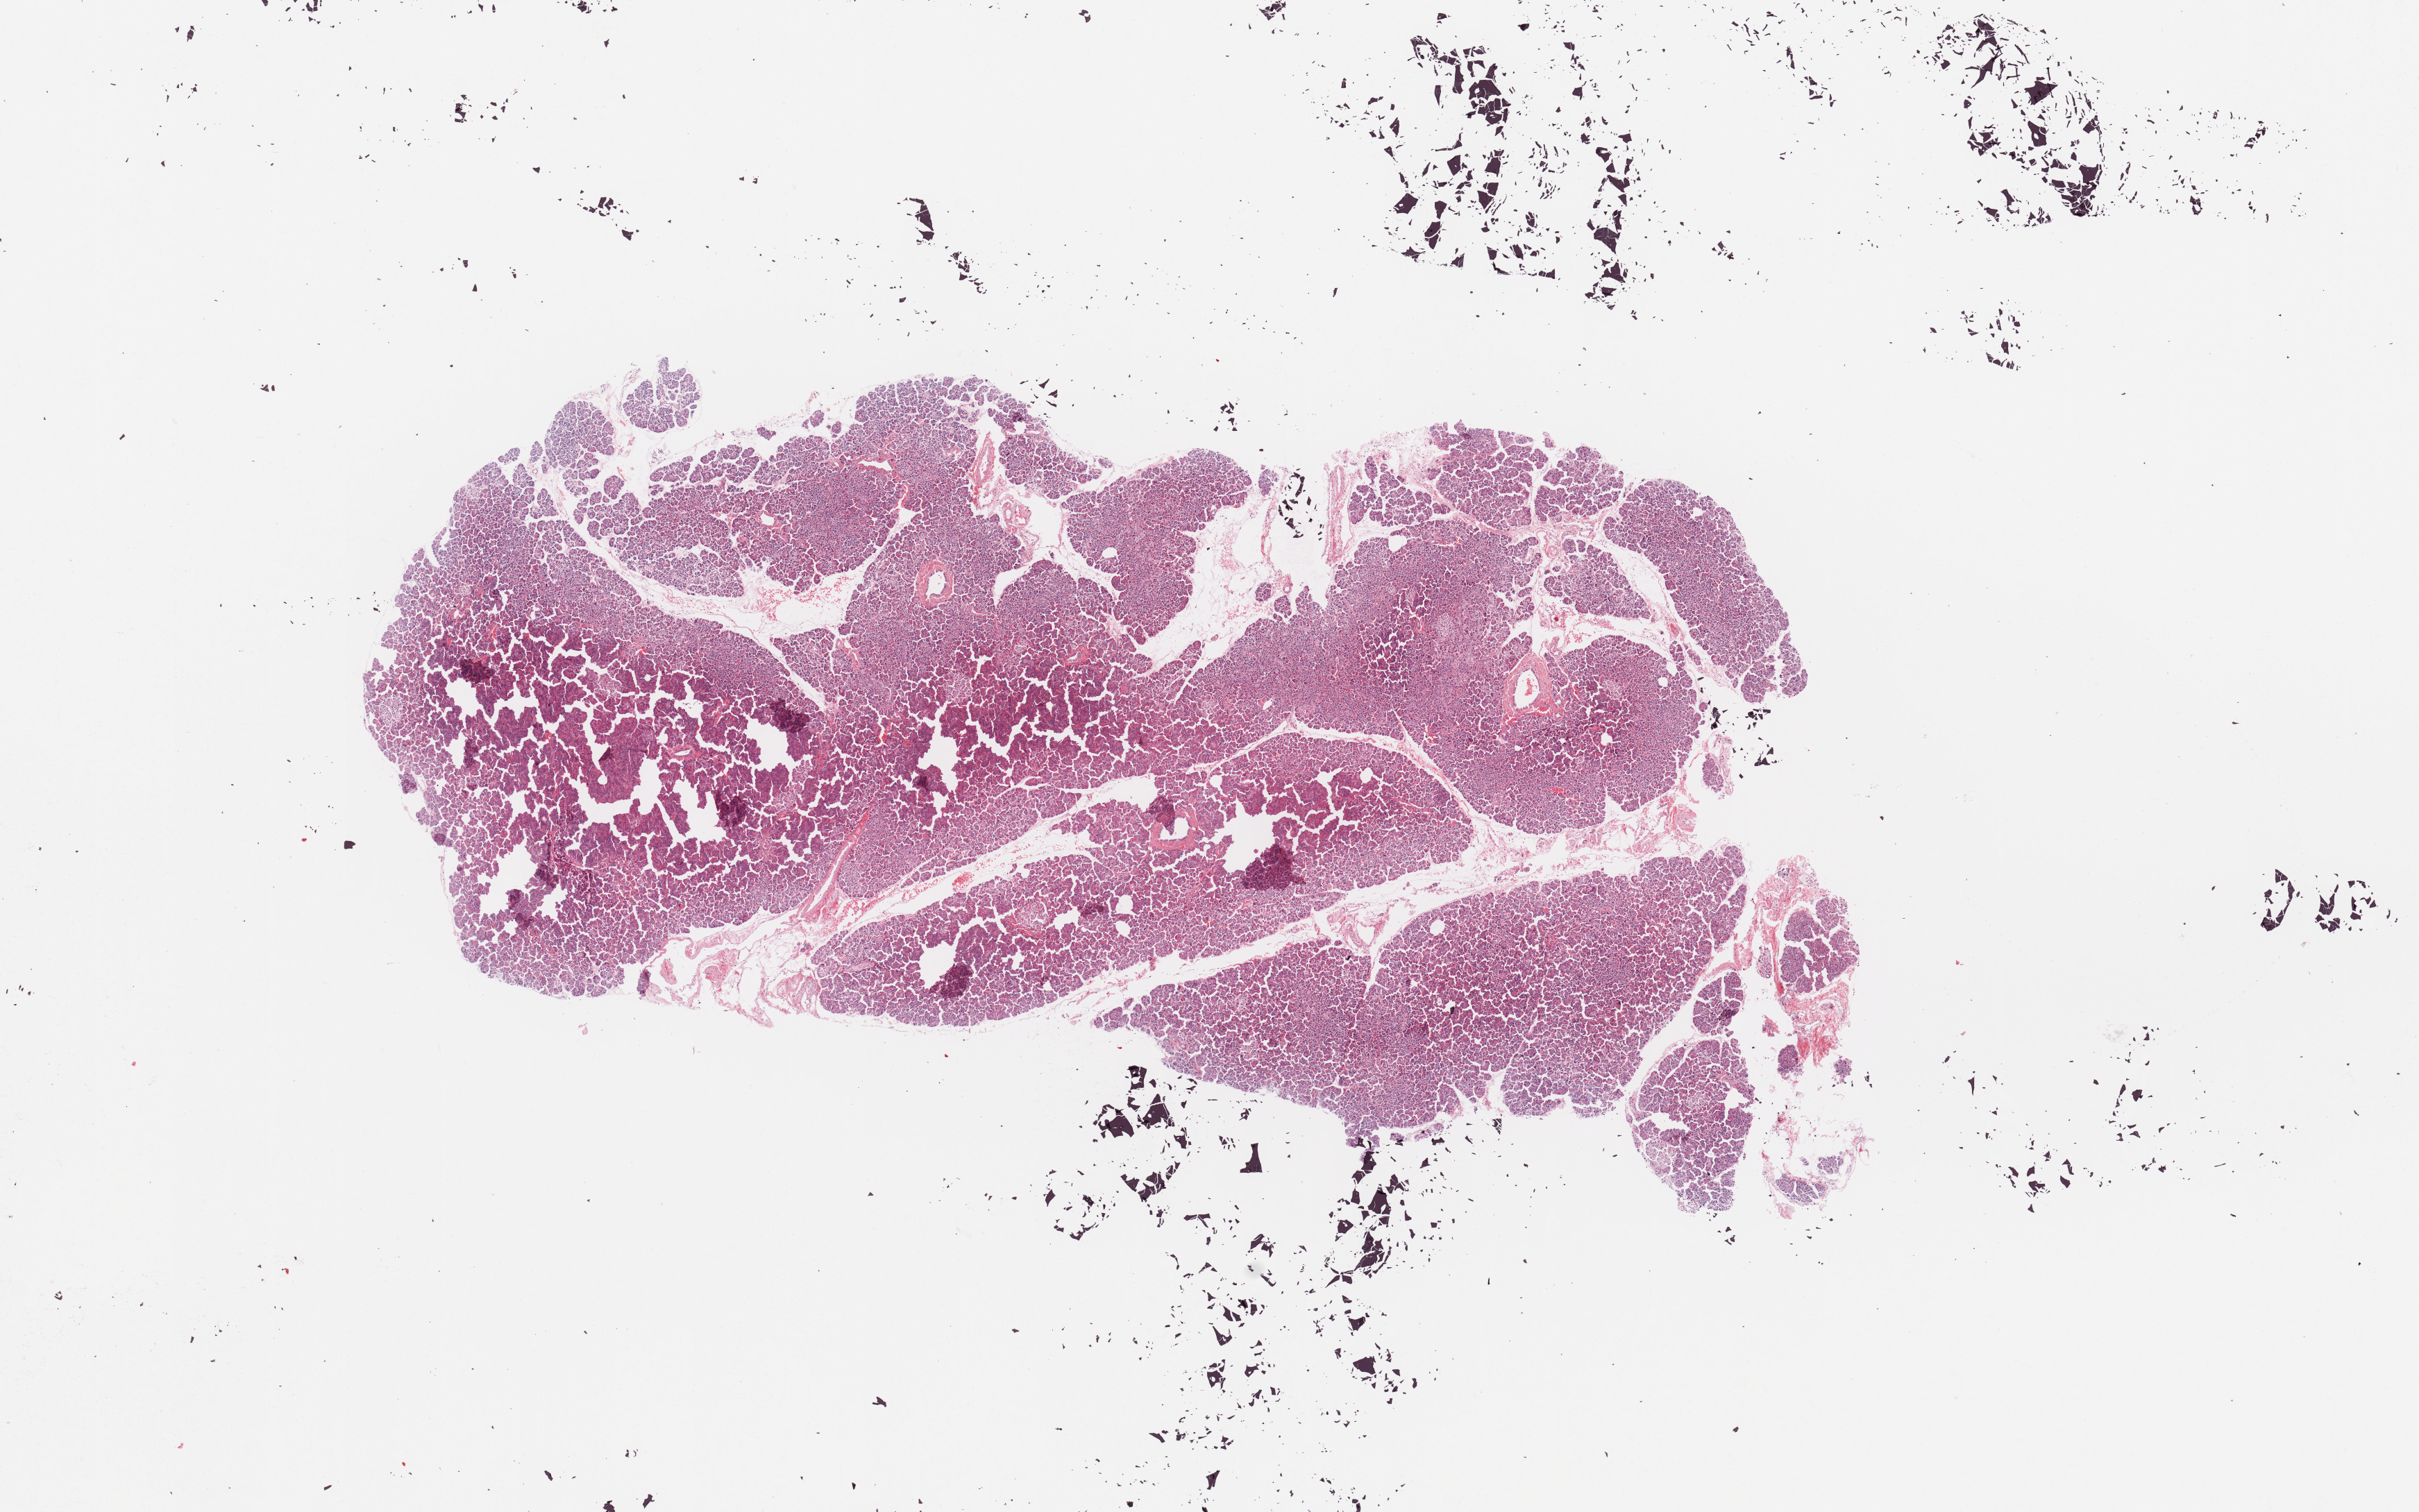
H&E whole-slide image — shown as a low-resolution overview of the whole scanned area (about 13.8 x 8.6 mm). Normal (non-tumour) tissue sample, sampled site: pancreas. 61-year-old female patient.
This section: normal (non-tumour) tissue from the same patient. Patient diagnosis: Infiltrating duct carcinoma, NOS.